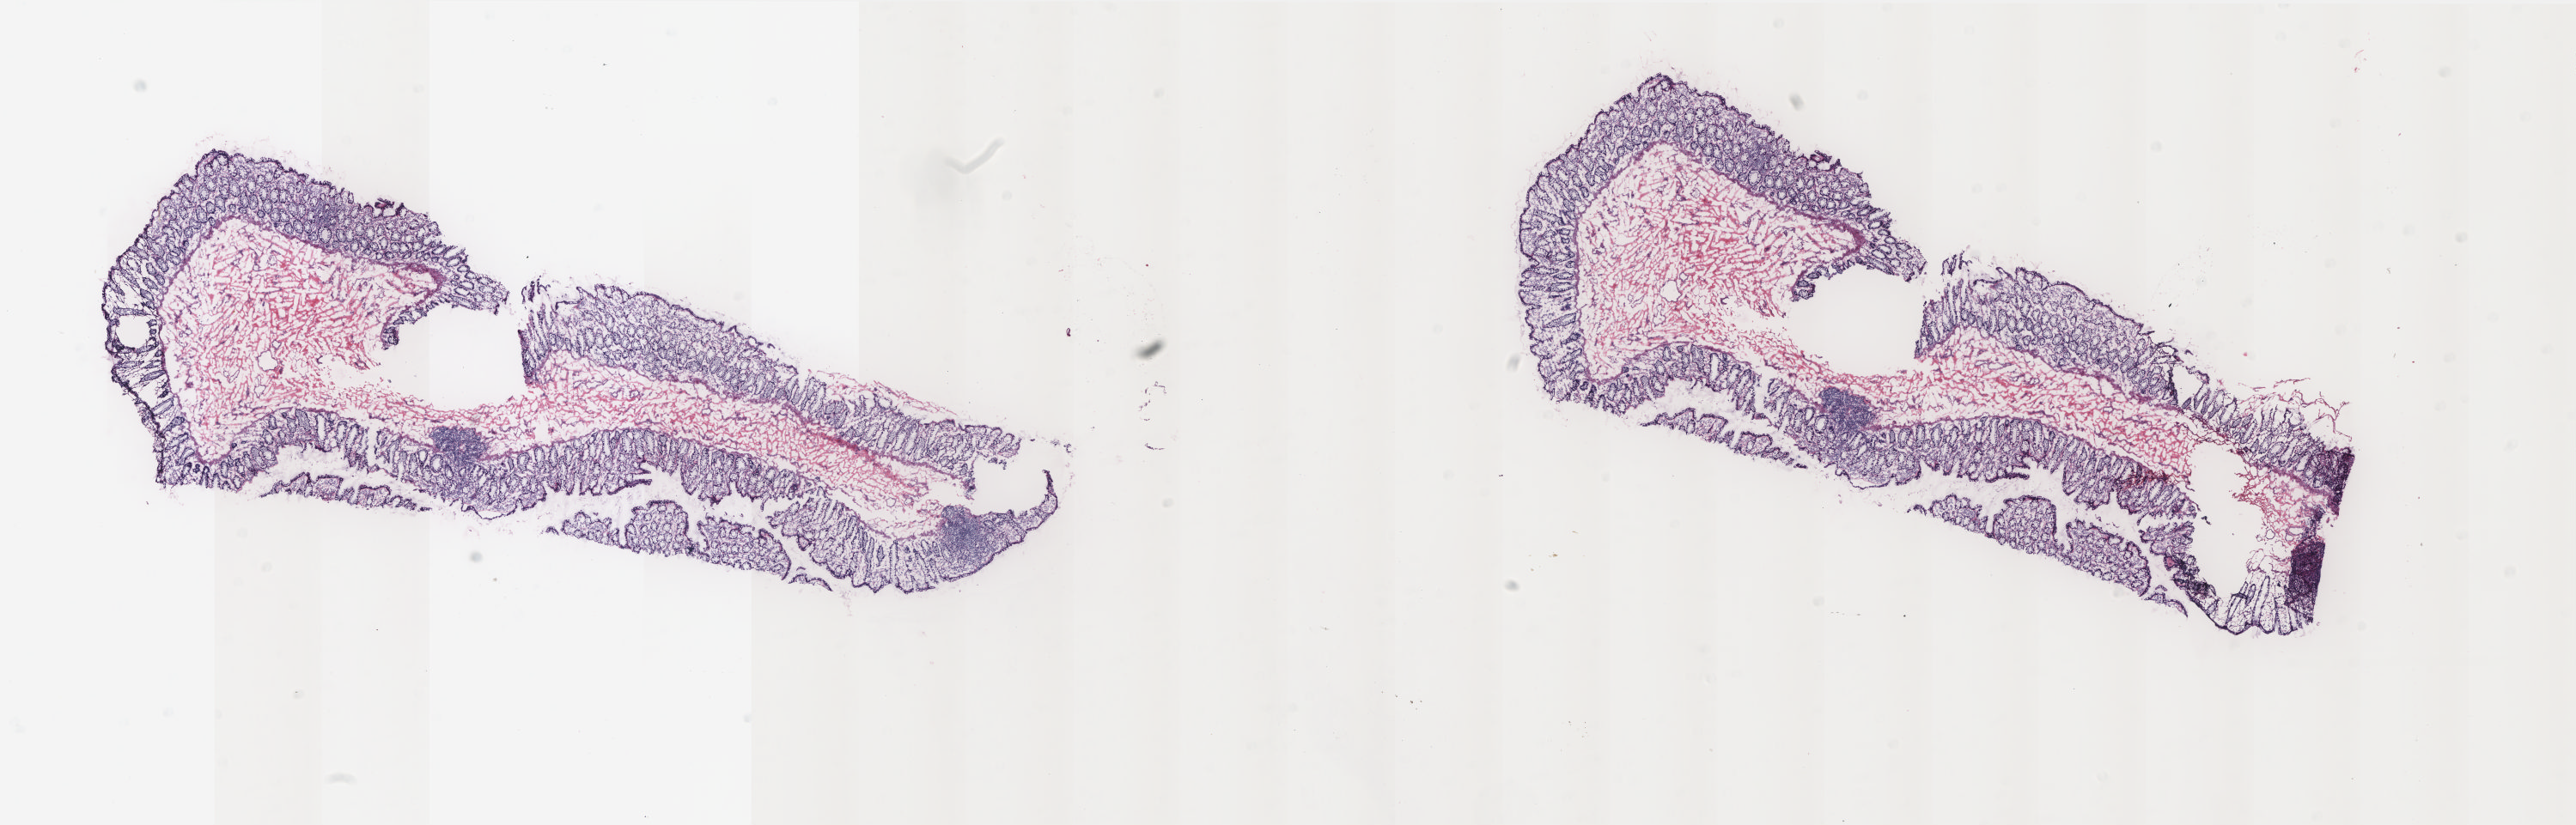
H&E whole-slide image, low-resolution overview of the scanned area, about 24.0 x 7.7 mm. Frozen section from the bottom of the tissue portion. Colon, solid tissue normal (non-tumour tissue) sample. Female patient; age at initial diagnosis 65 years. Pathologist review of this section (percent, as recorded): tumour cells 0%, normal cells 100%. Infiltration values recorded for this section: lymphocyte infiltration 35%, monocyte infiltration 6%, neutrophil infiltration 0%.
- this section: solid tissue normal sample (biorepository sample class)
- patient diagnosis: Adenocarcinoma, NOS (sigmoid colon)